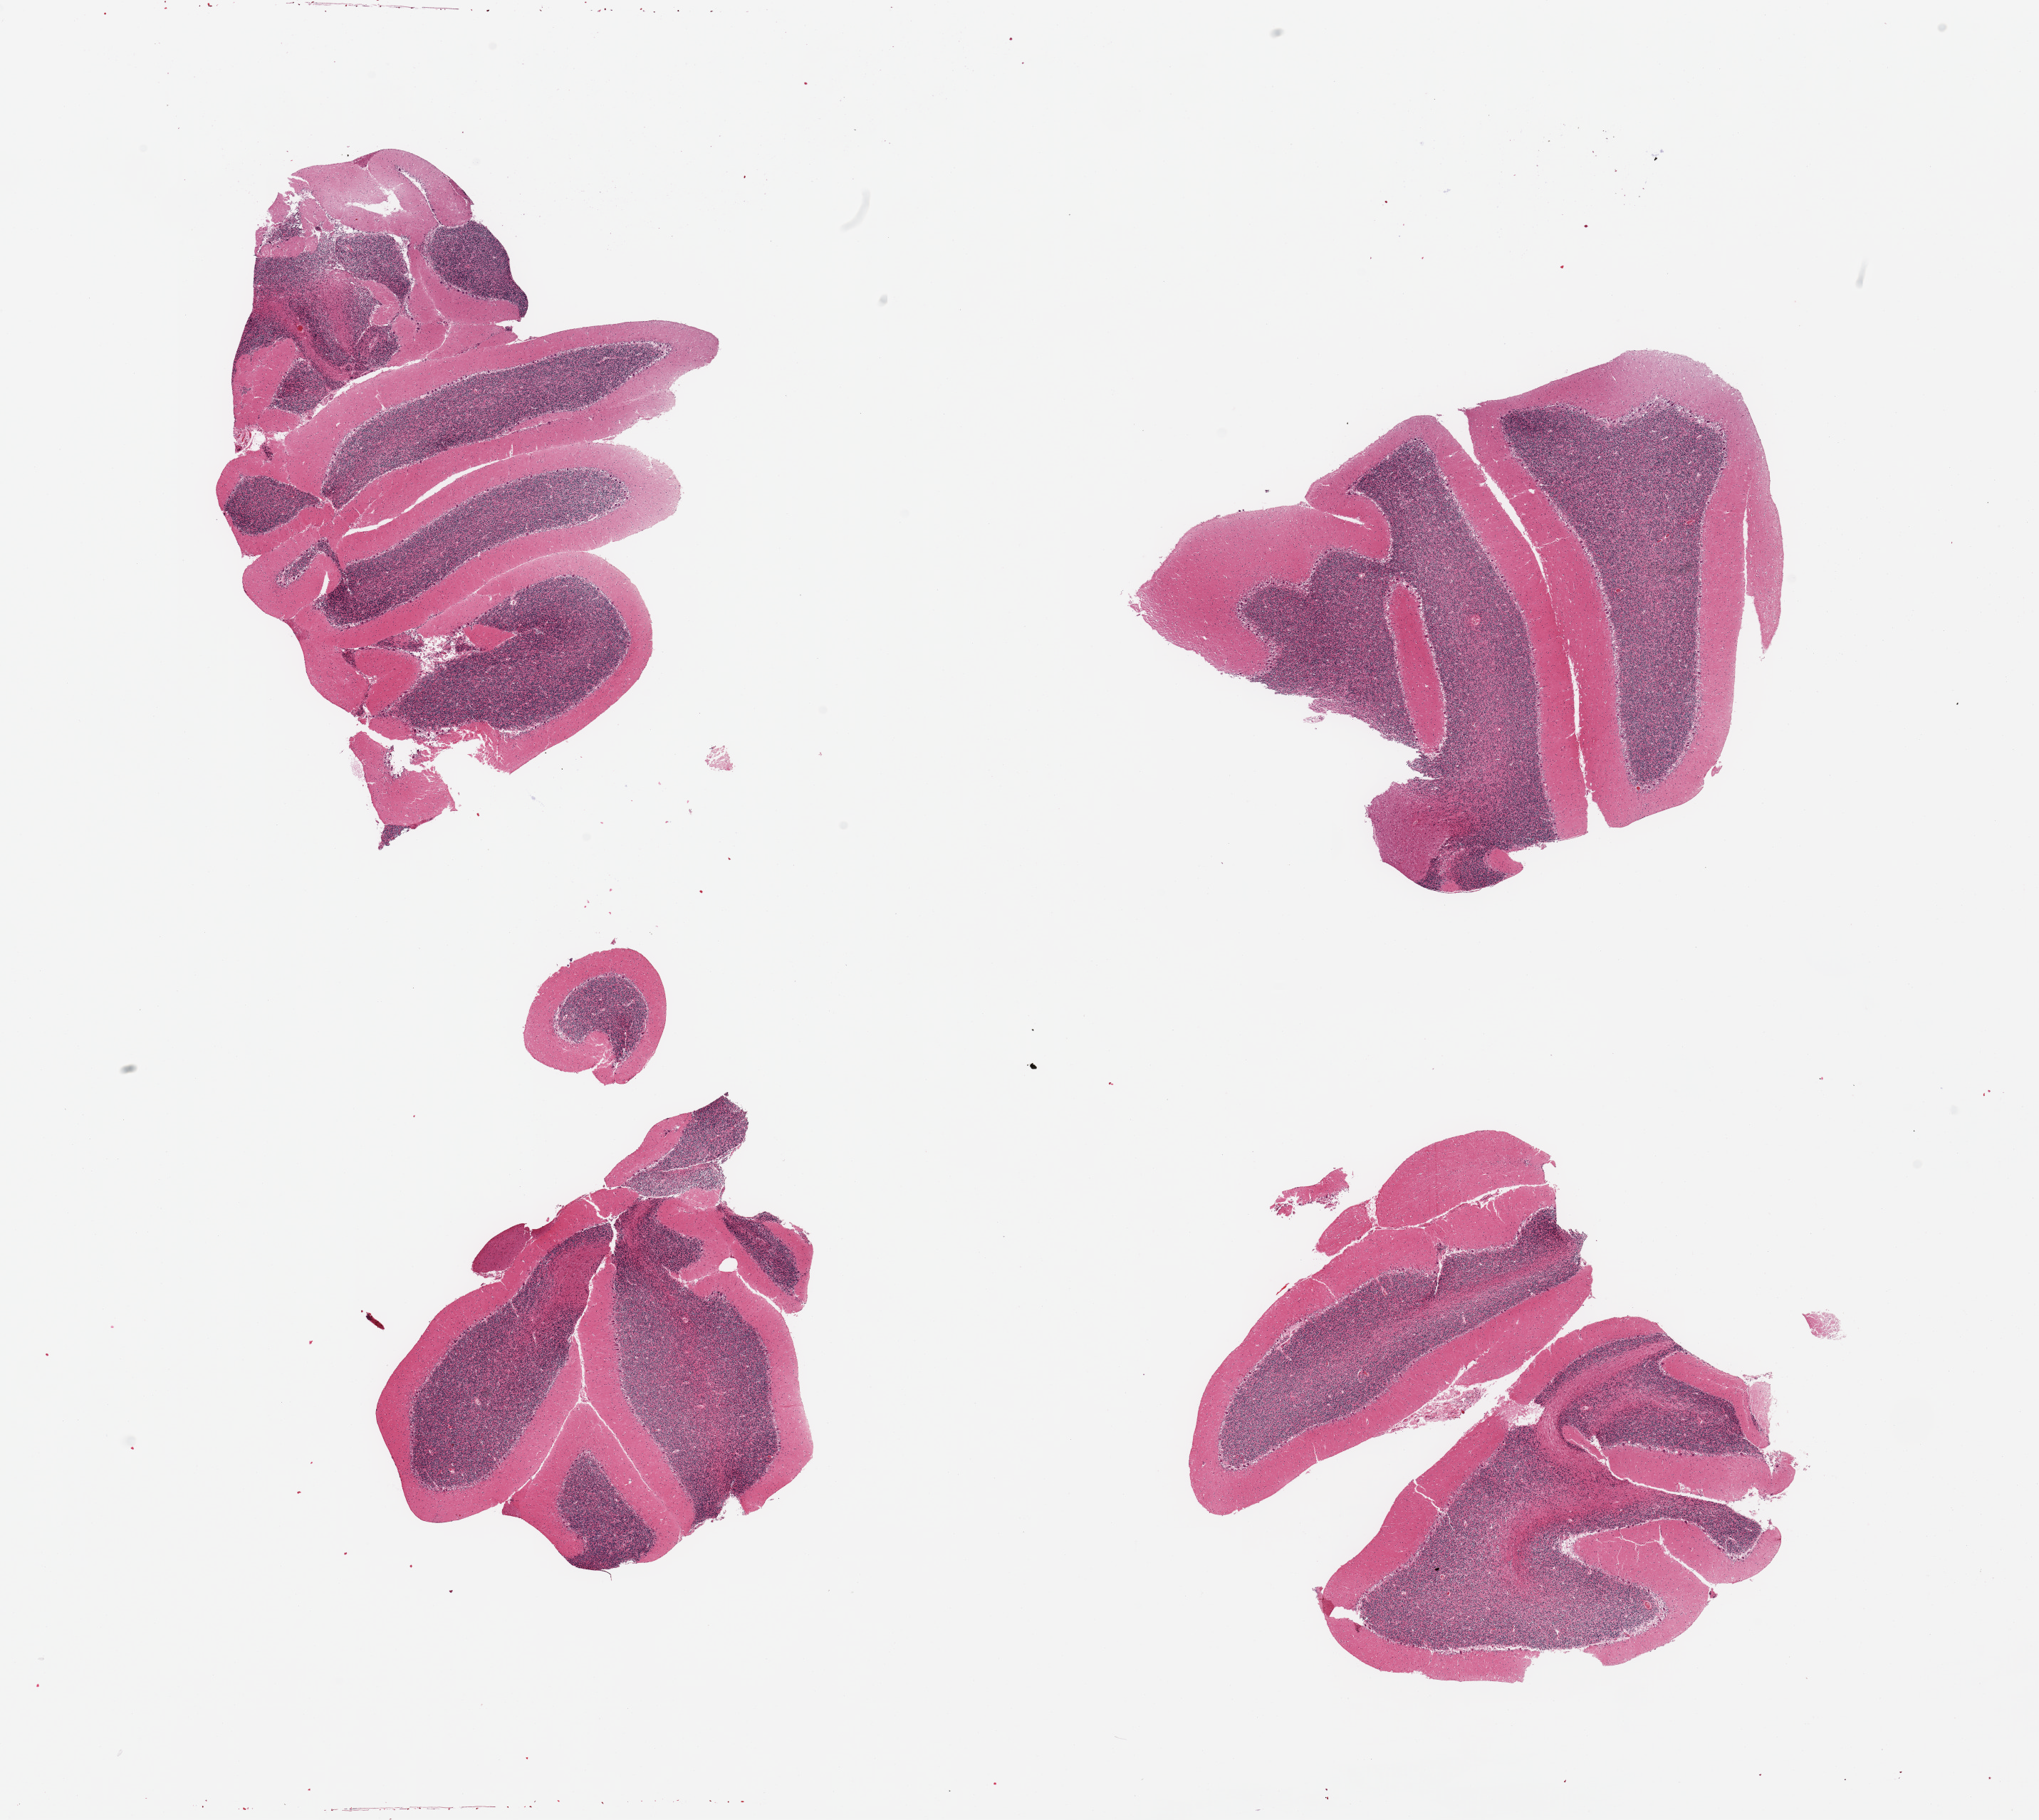
Digitized hematoxylin and eosin (H&E)-stained section — a low-resolution overview of the entire scanned area, about 22.6 x 20.2 mm (slide scanned at 20x), PAXgene-fixed paraffin-embedded (PFPE) section, section of cerebellum (target tissue), tissue donor sample. Donor: female.
Review note (as recorded): 4 pieces.